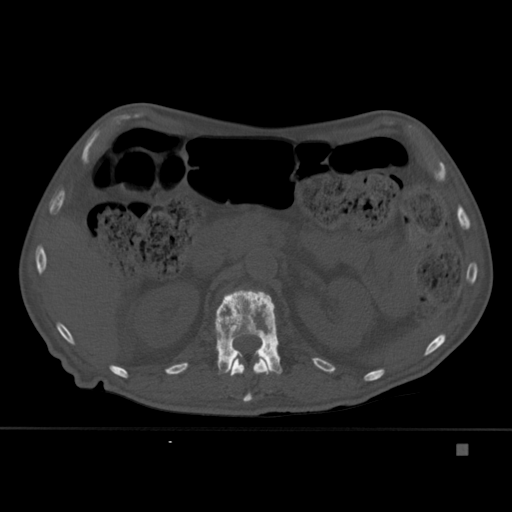
CT including the spine, one axial slice. Bone window (W 1800 / L 400 HU). 1.5 mm slice thickness. 512 × 512 image matrix, field of view 378 × 378 mm. Male patient, age 75 years. Case-level facts recorded for this patient, not image findings: primary cancer: prostate.
Structures marked on this image (semi-automatic segmentation, software-assisted and operator-edited):
- L1 vertebra: bounding box [x1, y1, x2, y2] px = [215, 289, 282, 375]
- T12 vertebra: [230, 355, 270, 402]